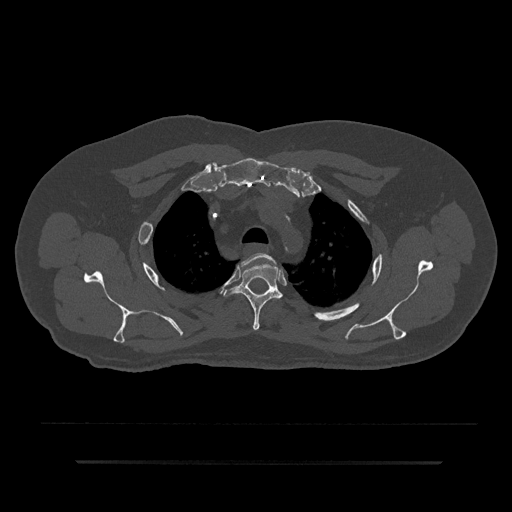
CT including the spine, one axial slice; position 660 of 797 along the scan axis; bone window (W 1800 / L 400 HU); 0.5 mm slice thickness; 512 × 512 image matrix, field of view 464 × 464 mm. Male patient, age 59 years. From the clinical record (not read from this slice): primary cancer: bile ducts.
Outlined on this slice (semi-automatic segmentation, software-assisted and operator-edited):
- T2 vertebra: bounding box <238,253,276,267> (left, top, right, bottom; pixels)
- T3 vertebra: <224,263,282,331>